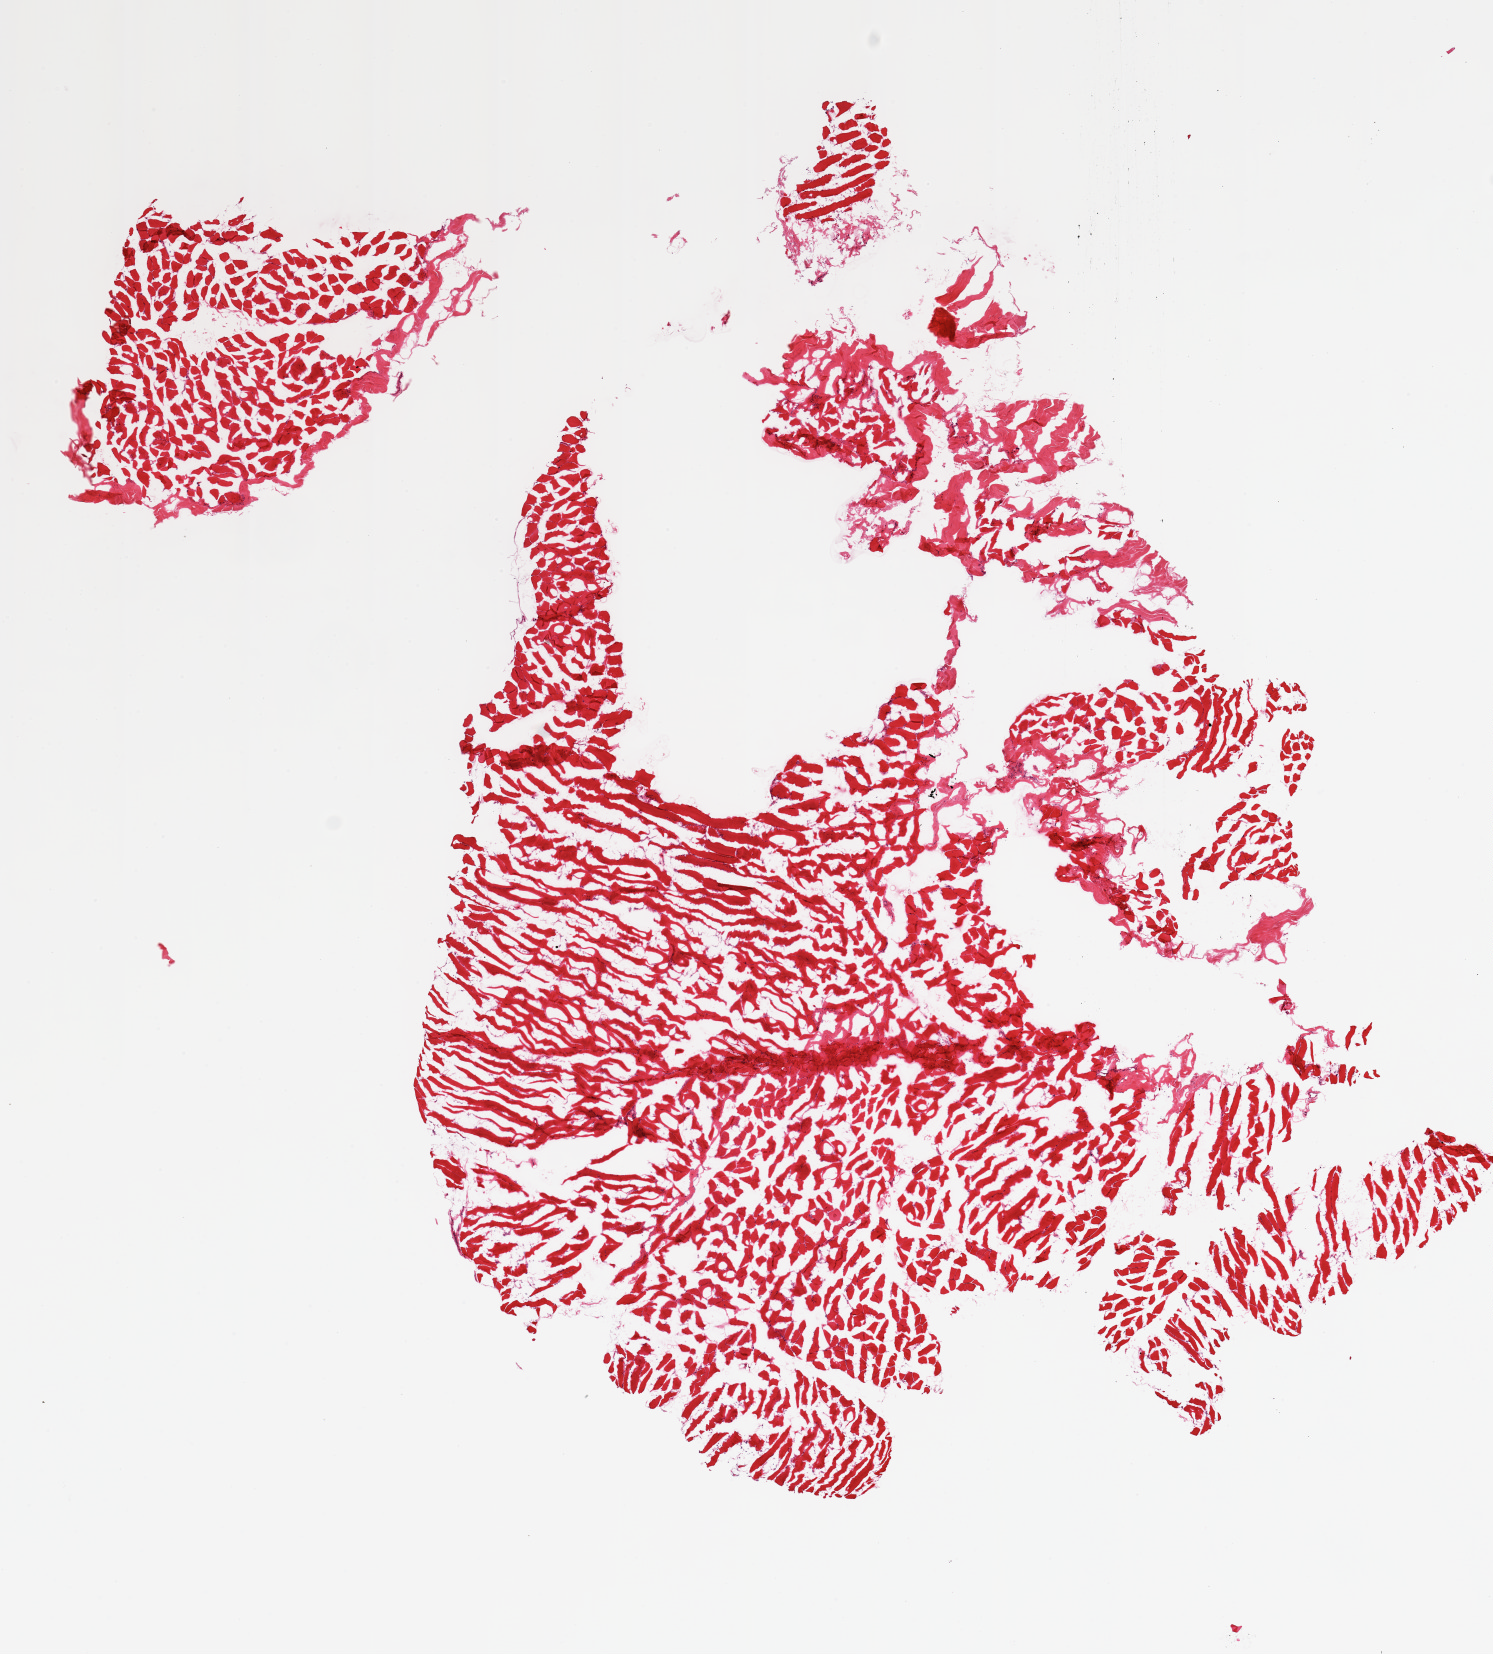
Hematoxylin and eosin (H&E) whole-slide image, brightfield — shown as a low-resolution overview of the whole scanned area (about 11.8 x 13.1 mm). Frozen section (dry ice). Target tissue: skeletal muscle. Donor tissue sample. Donor: female.
Review note (as recorded): 1 piece (fragmented).